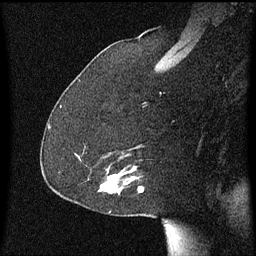
Breast MRI (dynamic contrast-enhanced), one sagittal slice; slice 39 of 60 in the series (ordered by position); dynamic contrast-enhanced series, image 2 of 3 at this slice position (ordered by acquisition); 1.5 T; TE 4.2 ms, TR 8.4 ms; 2 mm slice thickness; 256 × 256 image matrix, field of view 200 × 200 mm. Female patient, age 59 years.
Structures marked on this image (semi-automatic segmentation, software-assisted and operator-edited):
- analysis volume of interest (the breast-tissue region the enhancement analysis was run in; not a lesion): bounding box (x1, y1, x2, y2) in pixels: (98, 166, 143, 195)
- tumour enhancement mask (voxels above the 70 % enhancement threshold inside the analysis volume of interest): (108, 172, 143, 193)